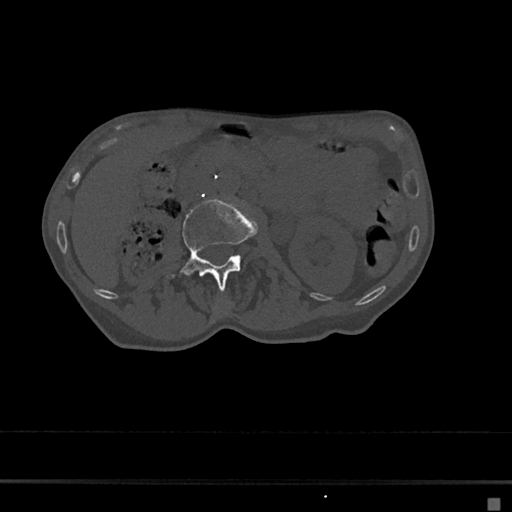
CT including the spine, one axial slice. Position 11 of 797 along the scan axis. Reconstruction kernel Br40s/3. 120 kVp. Bone window (W 1800 / L 400 HU). 0.5 mm slice thickness. 512 × 512 image matrix, field of view 360 × 360 mm. Patient: female, 68 years. From the clinical record (not read from this slice): primary cancer: renal.
Annotated regions visible in this slice (semi-automatically segmented with operator editing):
- L2 vertebra: box from (x=165, y=198) to (x=258, y=289) px